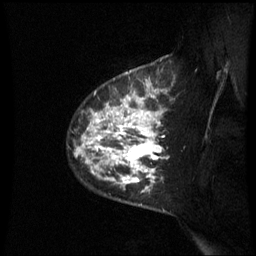
Breast MRI (dynamic contrast-enhanced), one sagittal slice. Position 48 of 60 along the scan axis. Dynamic contrast-enhanced series, image 2 of 3 at this slice position (ordered by acquisition). 1.5 T. TE 4.2 ms, TR 8.9 ms. 2.4 mm slice thickness. 256 × 256 image matrix, field of view 210 × 210 mm. Patient: female, 42 years. Case-level facts recorded for this patient, not image findings: setting: breast cancer imaged before/during neoadjuvant chemotherapy; receptor status: HER2-positive.
Structures marked on this image (semi-automatically segmented with operator editing):
- analysis volume of interest (the breast-tissue region the enhancement analysis was run in; not a lesion): box from (x=77, y=93) to (x=165, y=210) px
- tumour enhancement mask (voxels above the 70 % enhancement threshold inside the analysis volume of interest): (x=79, y=93)–(x=164, y=193)